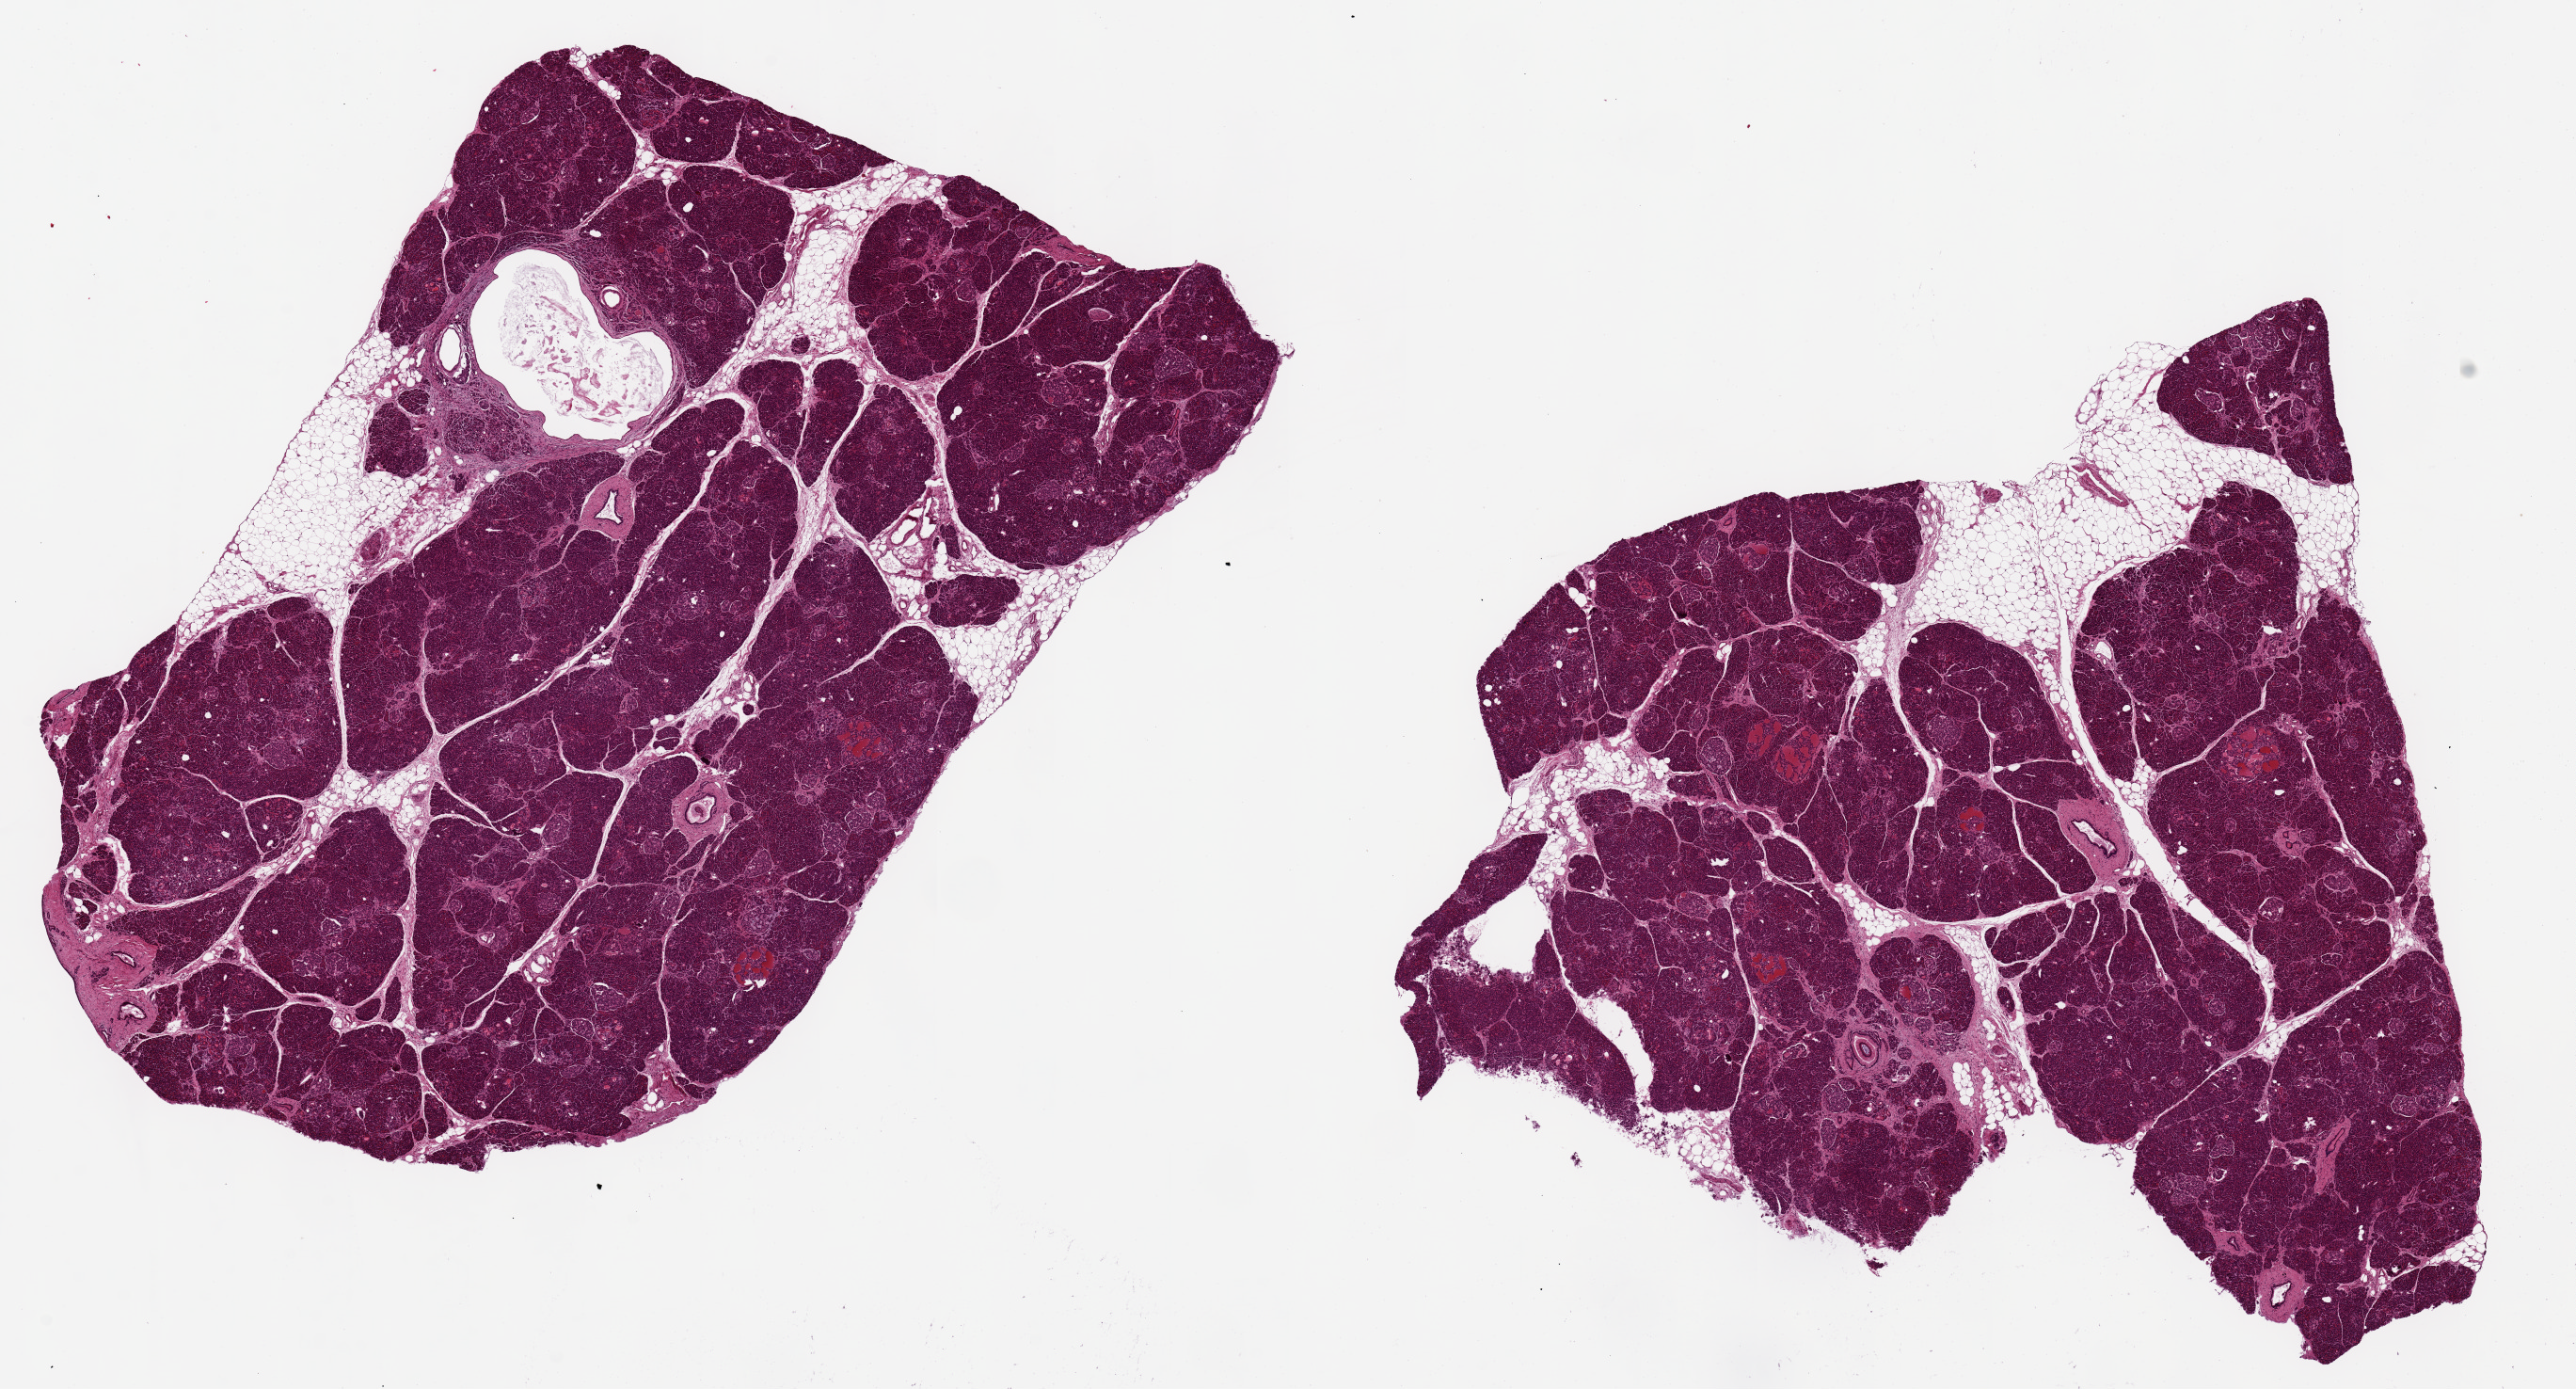
Whole-slide image, haematoxylin and eosin stain — a low-resolution overview of the entire scanned area, about 21.7 x 11.7 mm; PAXgene-fixed, paraffin-embedded tissue; target tissue: pancreas; tissue donor sample. Donor sex: male.
Pathologist's review note for this sample: 2 pieces 9.7x7 & 8.5x8.3 mm; good preservation; islets ~250 um; ~10% adipose.